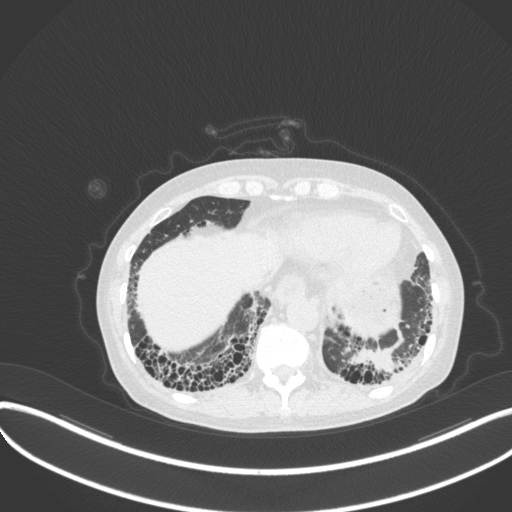
Chest CT, one axial slice. Position 61 of 373 along the scan axis. Lung window (W 1500 / L -600 HU). 512 × 512 image matrix, field of view 400 × 400 mm. Patient: female, 56 years. From the clinical record (not read from this slice): clinical TNM (as recorded): T1 N0 M0.
Annotated regions visible in this slice (bounding box drawn by a radiologist):
- lung tumour (recorded histology: adenocarcinoma): bounding box [x1, y1, x2, y2] px = [347, 347, 402, 378]